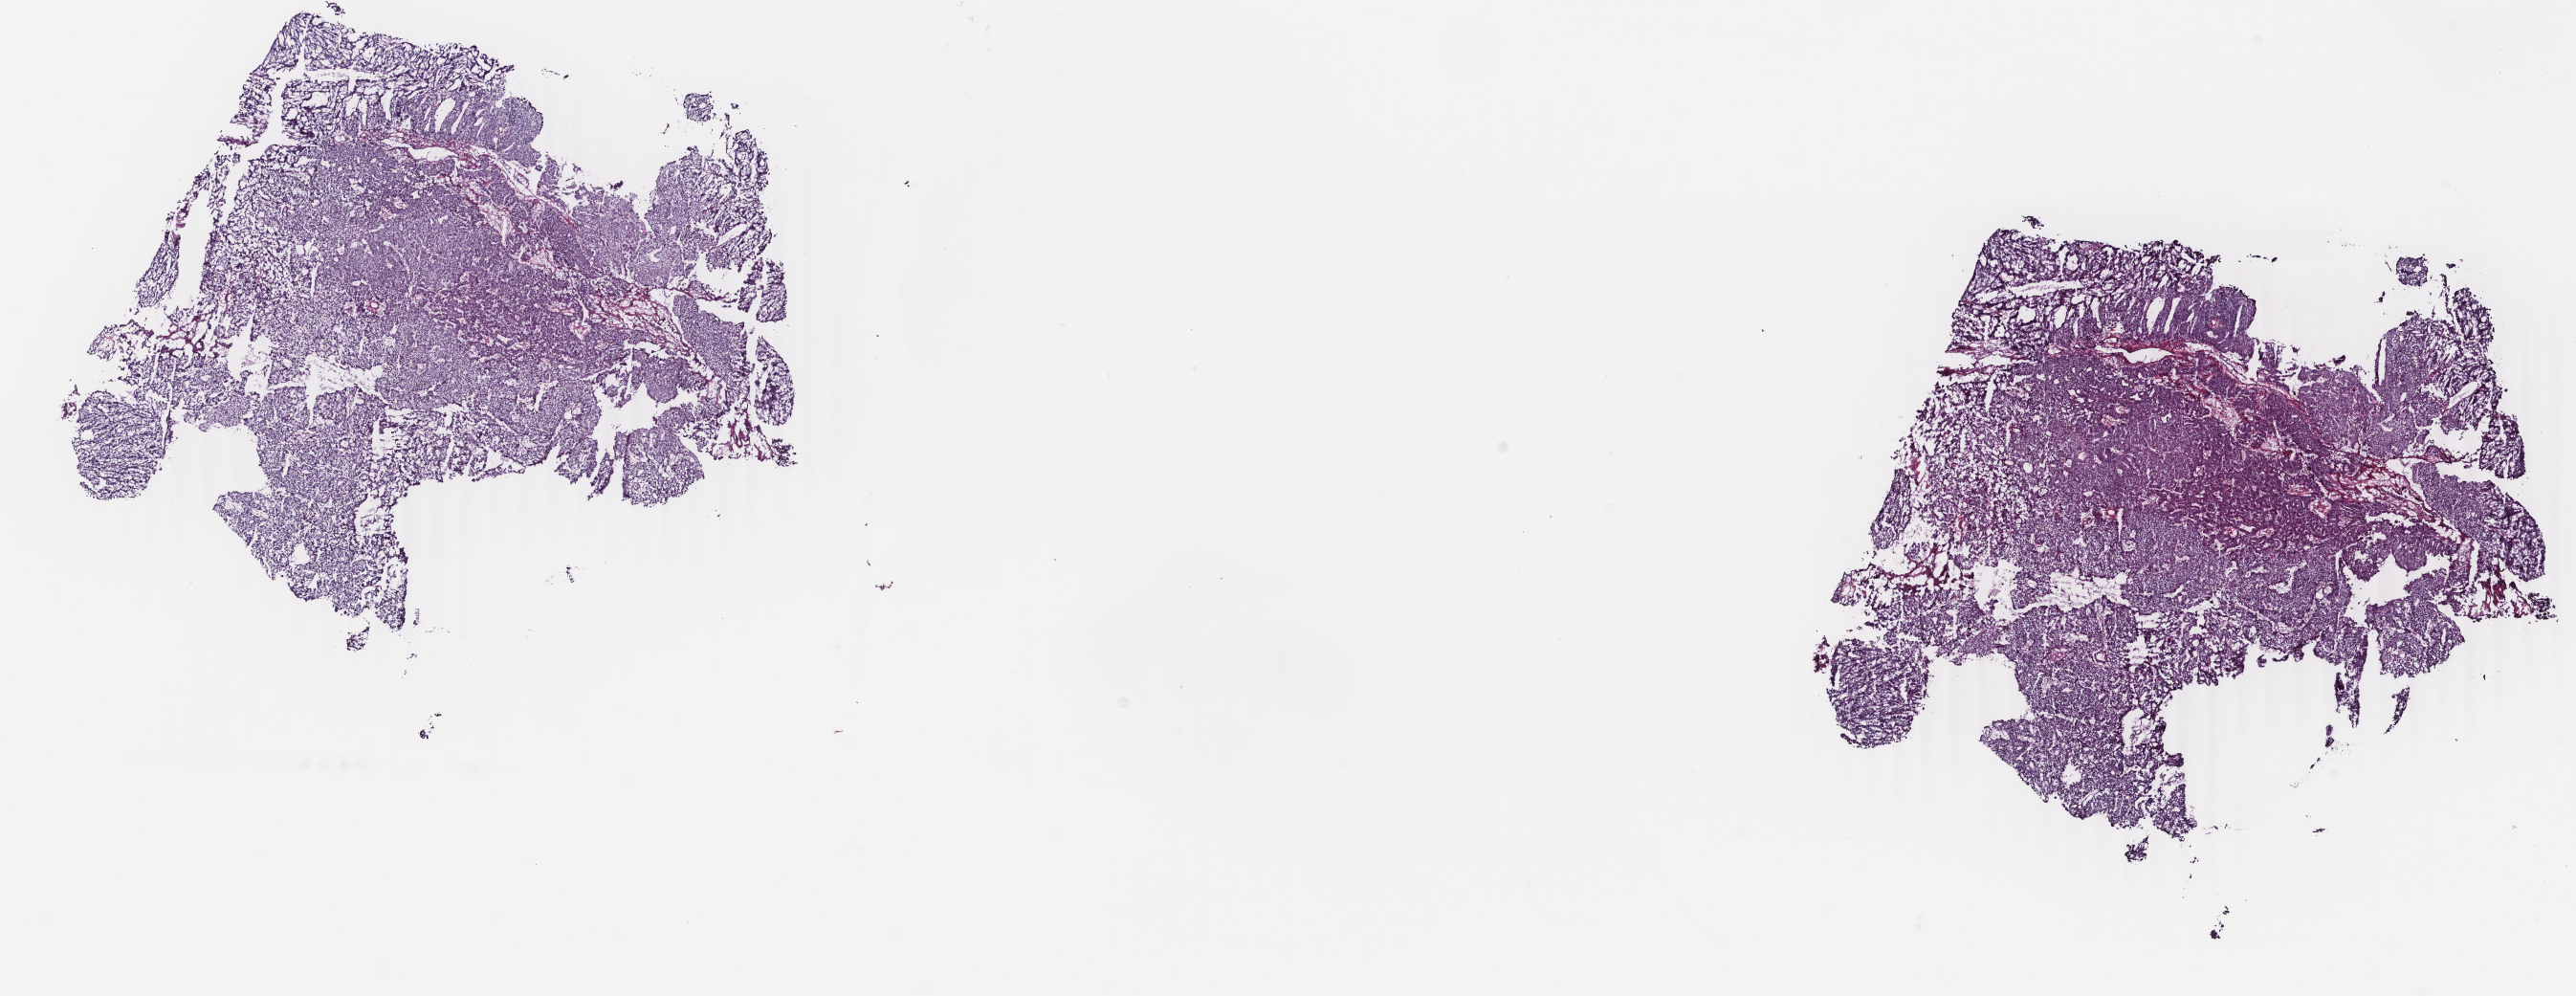
Digitized H&E tissue section (whole slide), a low-resolution overview of the entire scanned area, about 21.4 x 8.3 mm (slide scanned at 40x); frozen section from the top of the tissue portion; sample: primary tumour, uterus. Female patient; age at initial diagnosis 57 years. Histologic grade: G2 (moderately differentiated). Pathologist review of this section (percent, as recorded): tumour cells 90%, tumour nuclei 90%, normal cells 0%, stromal cells 10%, necrosis 0%. Inflammatory infiltration, as recorded: lymphocyte infiltration 3%, monocyte infiltration 0%, neutrophil infiltration 0%.
Pathologic diagnosis: Endometrioid adenocarcinoma, NOS (endometrium). FIGO stage: IB.